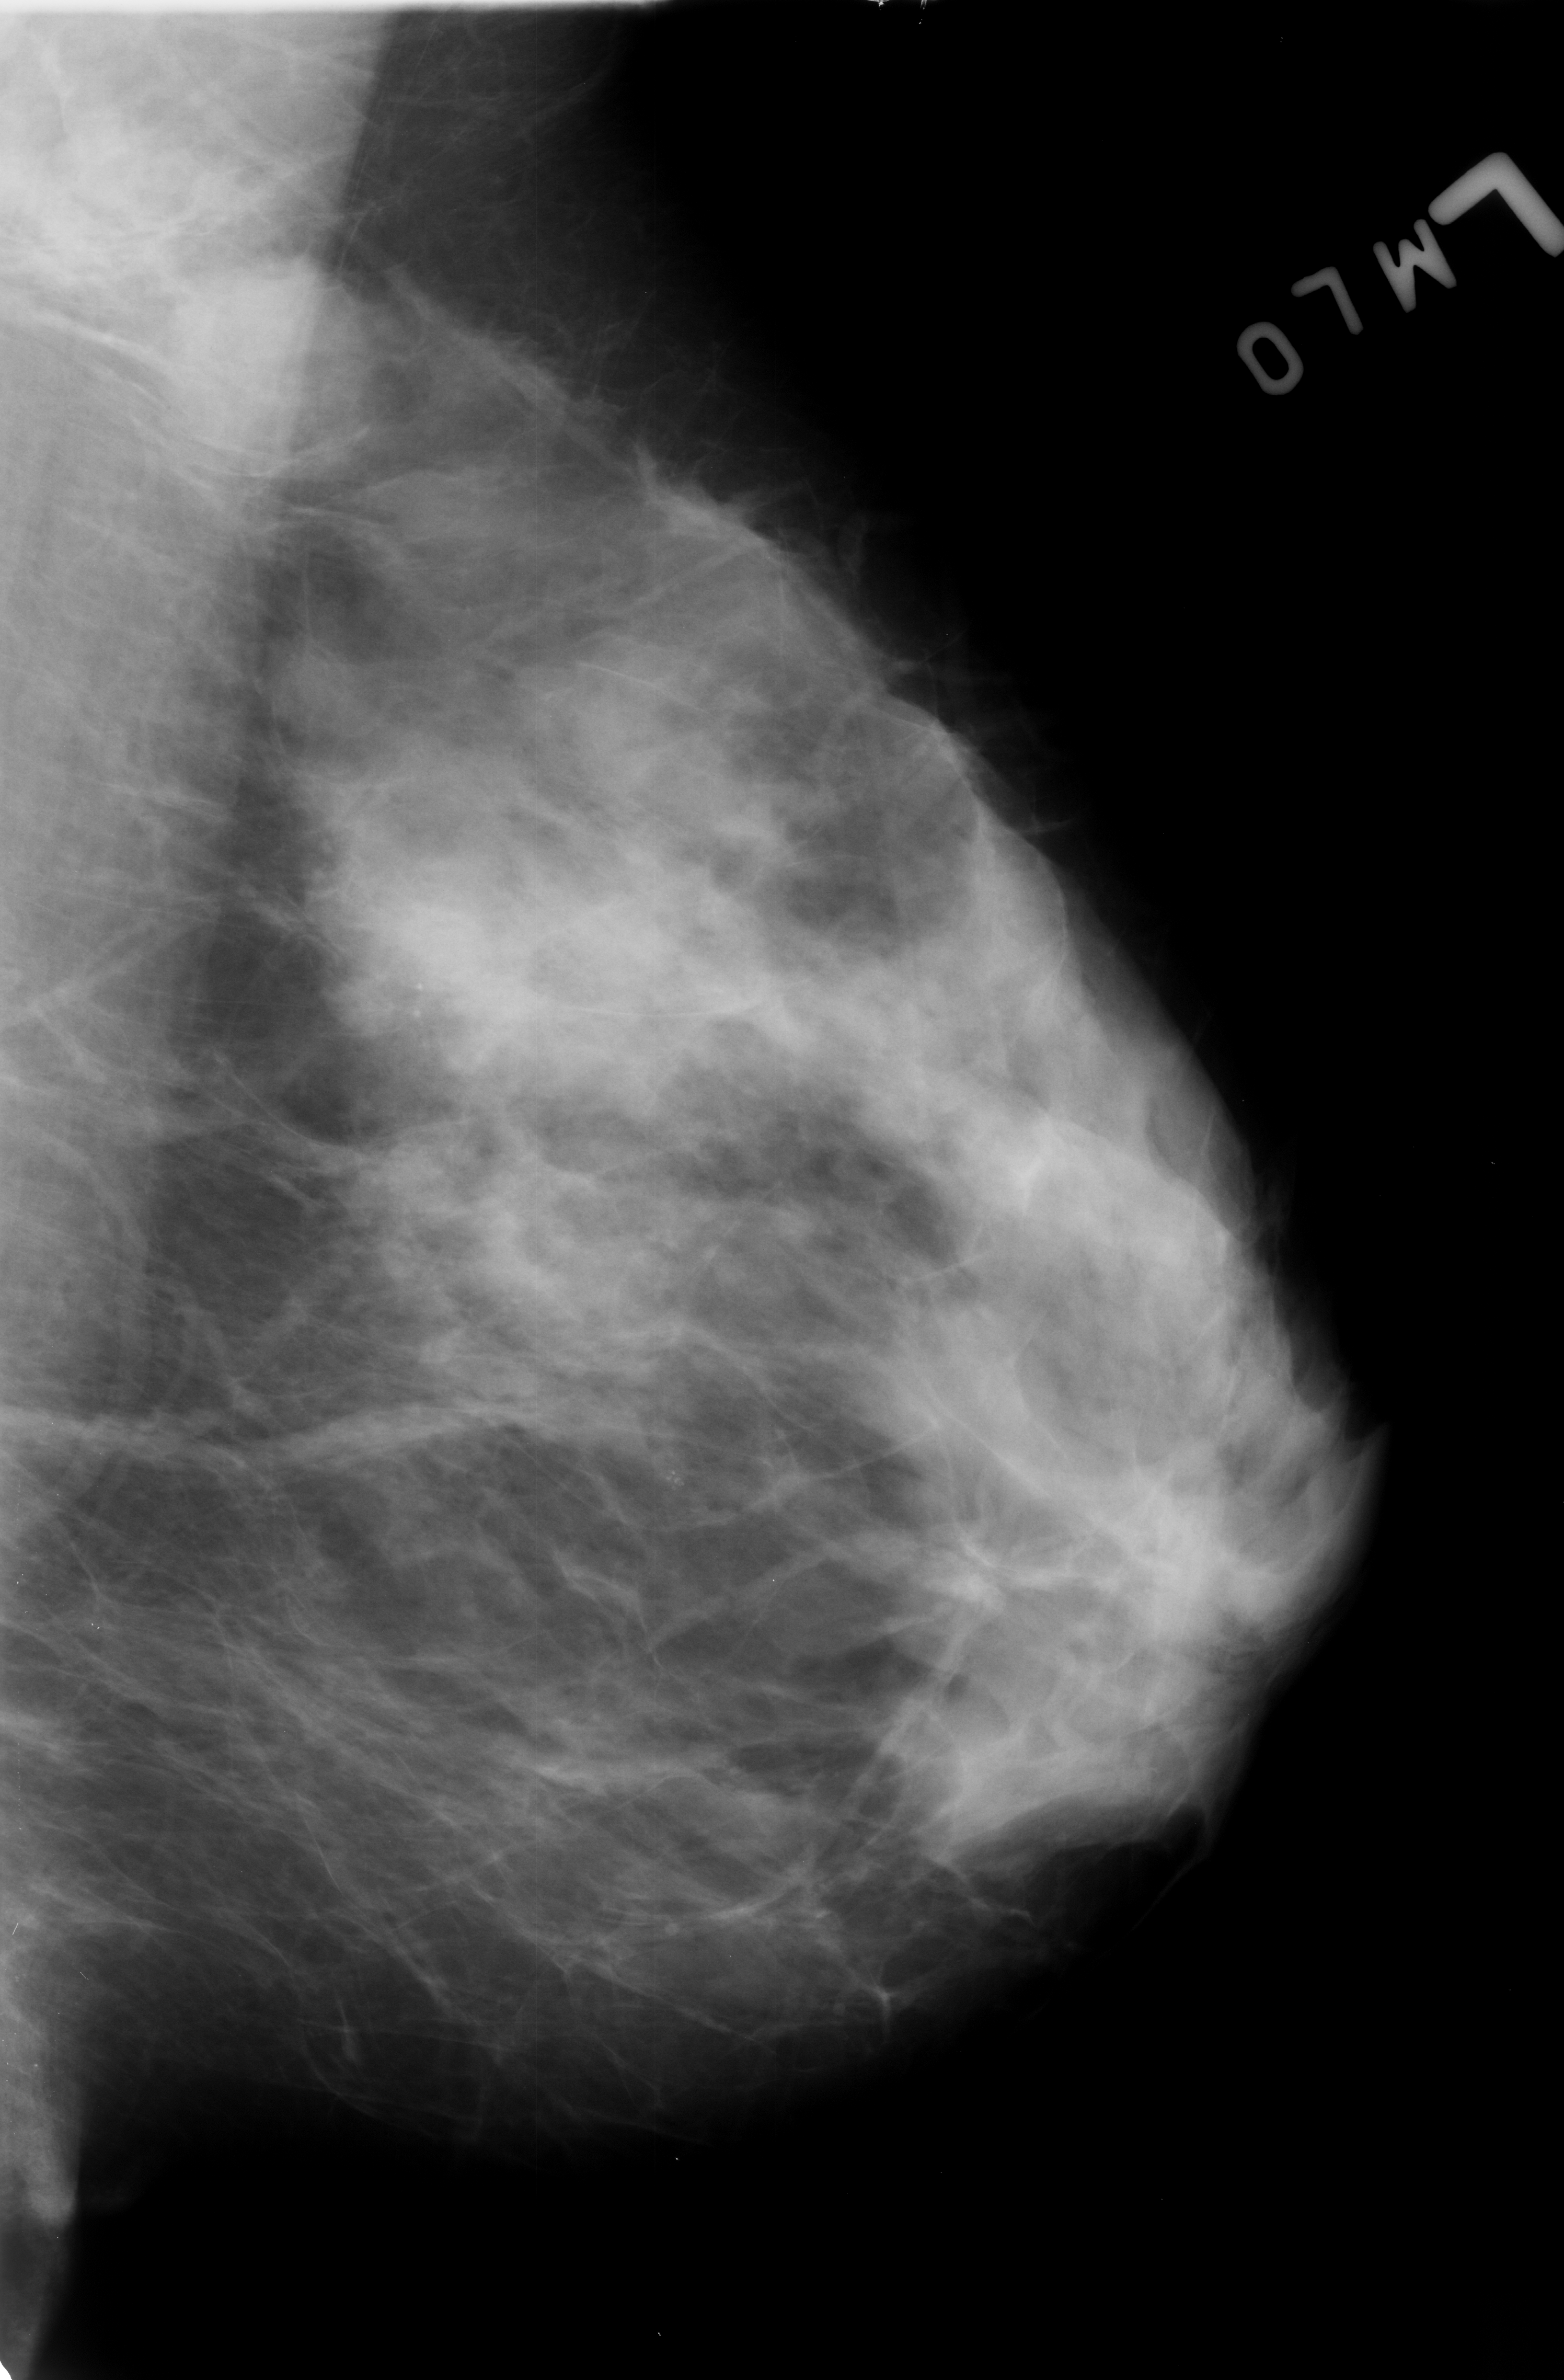
Scanned film-screen mammogram; left breast; MLO view; breast composition: heterogeneously dense (BI-RADS density category 3 of 4); 1564 × 2380 image matrix.
Expert-marked regions of interest on this film, with their recorded descriptors:
- calcifications, morphology pleomorphic, distribution clustered; BI-RADS assessment category 4; subtlety rating 3 on a 1 (subtle) to 5 (obvious) scale; pathology result (as recorded, not read from the image): benign: bounding box [x1, y1, x2, y2] px = [598, 1422, 745, 1540]